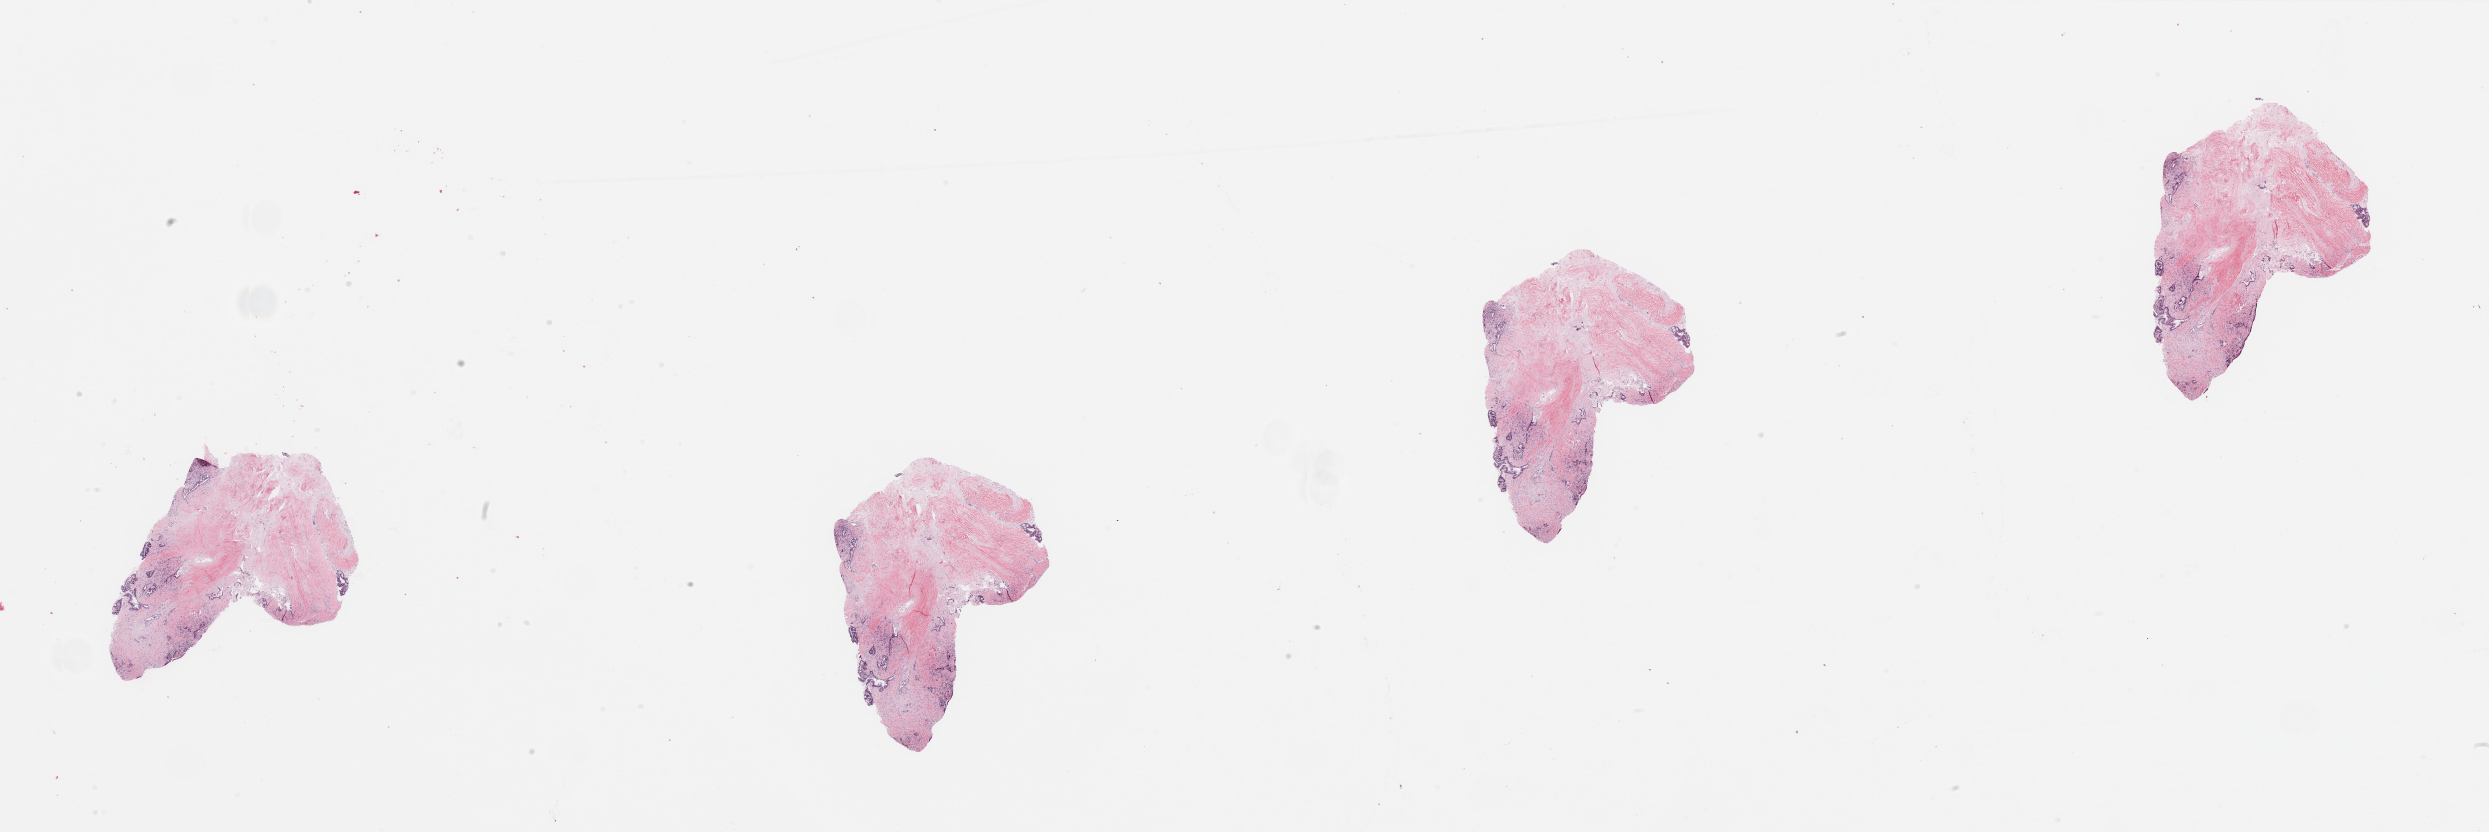
Whole-slide histology image, H&E-stained, shown as a low-resolution overview of the whole scanned area (about 39.4 x 13.2 mm, acquisition: 20x scan); pancreas, tumour tissue. 34-year-old female patient. Histologic grade: G2 (moderately differentiated).
• diagnosis: Infiltrating duct carcinoma, NOS
• AJCC pathologic stage: IIB
• primary tumour site (as recorded): head